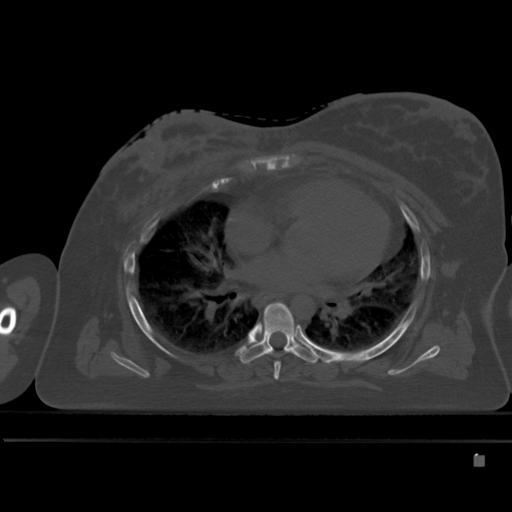
CT including the spine, one axial slice; slice 310 of 495 in the series (ordered by position); bone window (W 1800 / L 400 HU); 1.5 mm slice thickness; 512 × 512 image matrix, field of view 404 × 404 mm. Female patient, age 33 years. Case-level facts recorded for this patient, not image findings: primary cancer: breast.
Annotated regions visible in this slice (semi-automatic segmentation, software-assisted and operator-edited):
- T5 vertebra: bounding box [x1, y1, x2, y2] px = [273, 362, 280, 380]
- T6 vertebra: [240, 302, 320, 364]